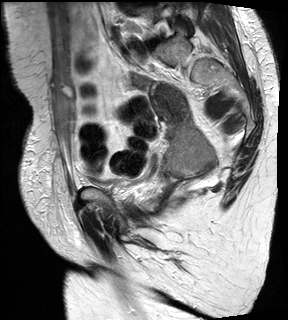
Pelvic MRI for cervical cancer, one sagittal slice; T2-weighted; 1.5 T; TE 89 ms, TR 2740 ms; 288 × 320 image matrix, field of view 234 × 260 mm. Female patient, age 59 years.
Outlined on this slice (outlined manually by an expert reader):
- uterus and cervix: bounding box (x1, y1, x2, y2) in pixels: (147, 81, 217, 179)